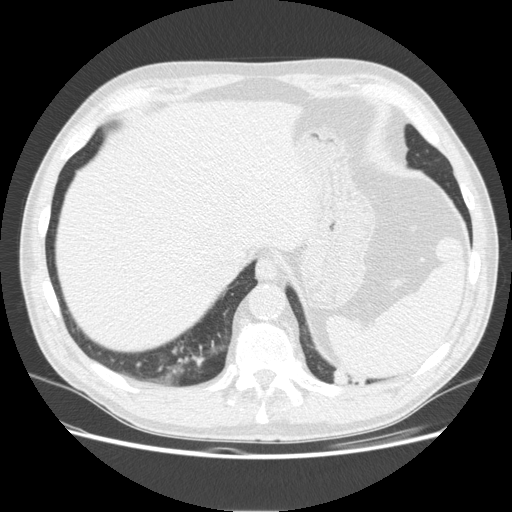
Low-dose screening chest CT, one axial slice. 120 kVp. Lung window (W 1500 / L -600 HU). 2.5 mm slice thickness. 512 × 512 image matrix, field of view 375 × 375 mm.
Annotated regions visible in this slice (manually delineated by an expert):
- lesion 1 (tumor, upper lobe of left lung): bounding box [x1, y1, x2, y2] px = [333, 368, 366, 384]